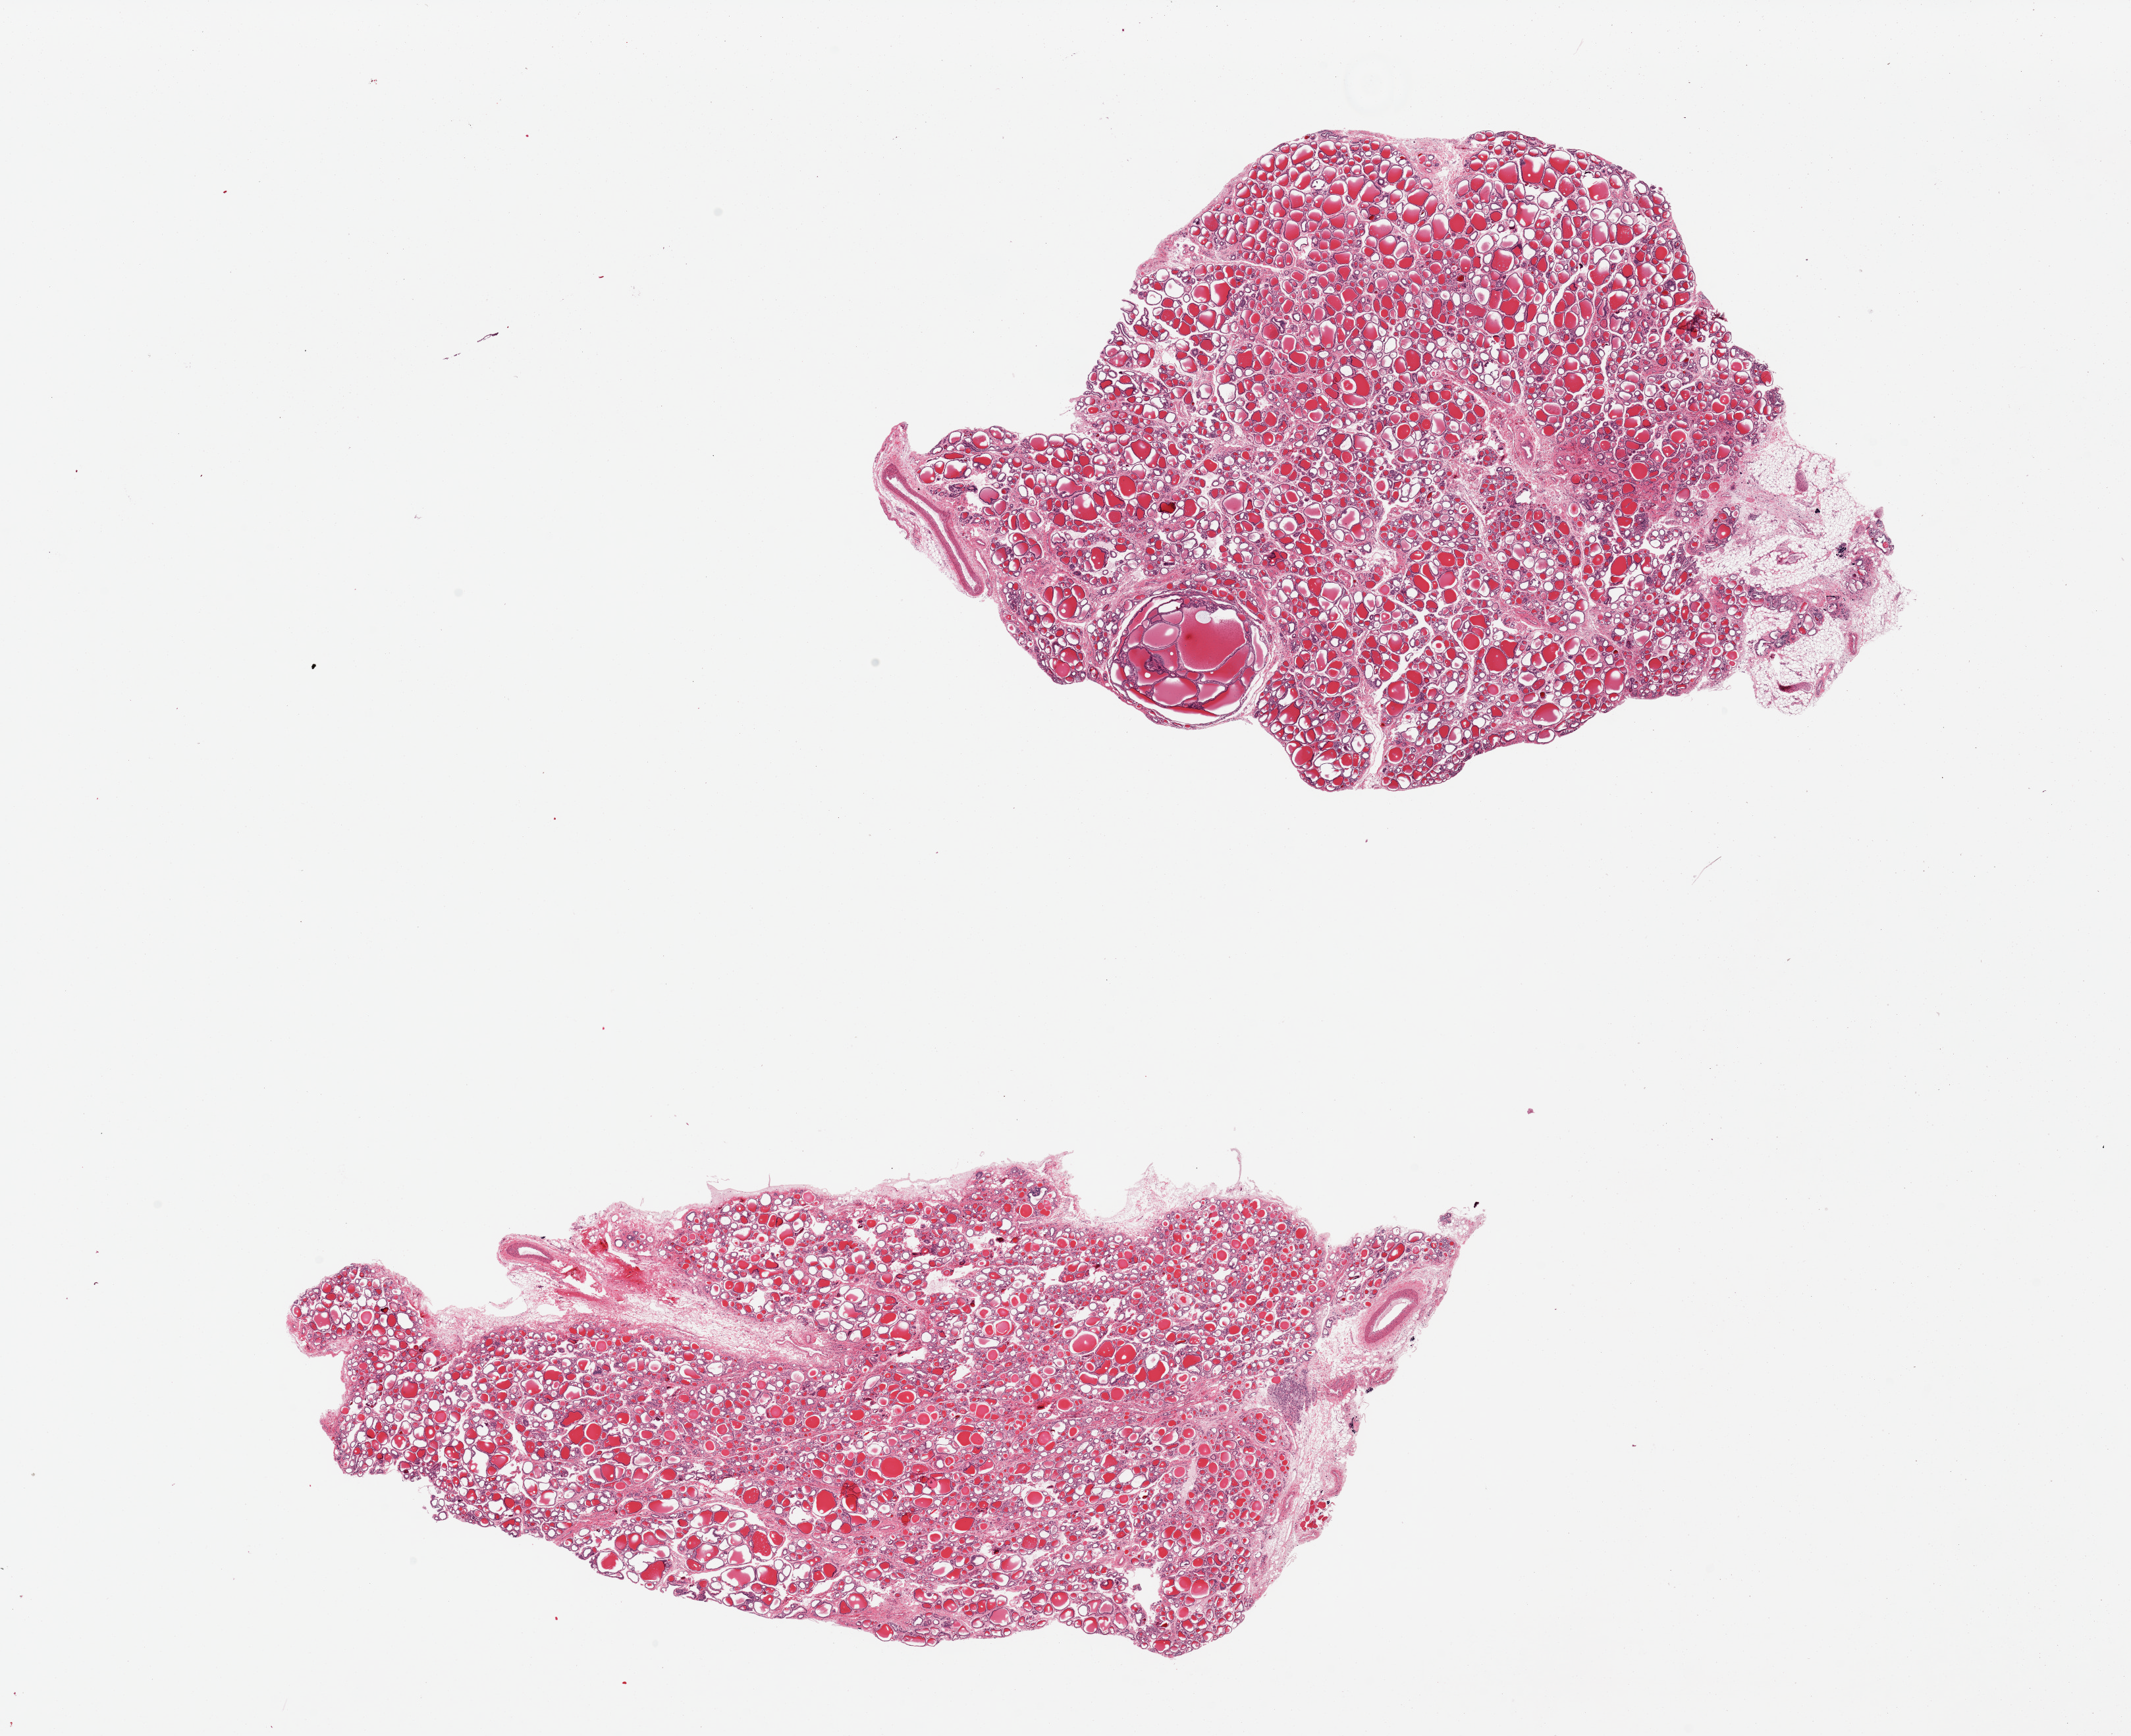
Whole-slide image, haematoxylin and eosin stain, whole scanned area (about 25.6 x 20.8 mm) shown as a low-resolution overview. PAXgene-fixed paraffin-embedded (PFPE) section. Target tissue: thyroid. Donor tissue sample. Female donor.
Pathologist's review note for this sample: 2 pieces, one piece includes ~10% fat and nerve.